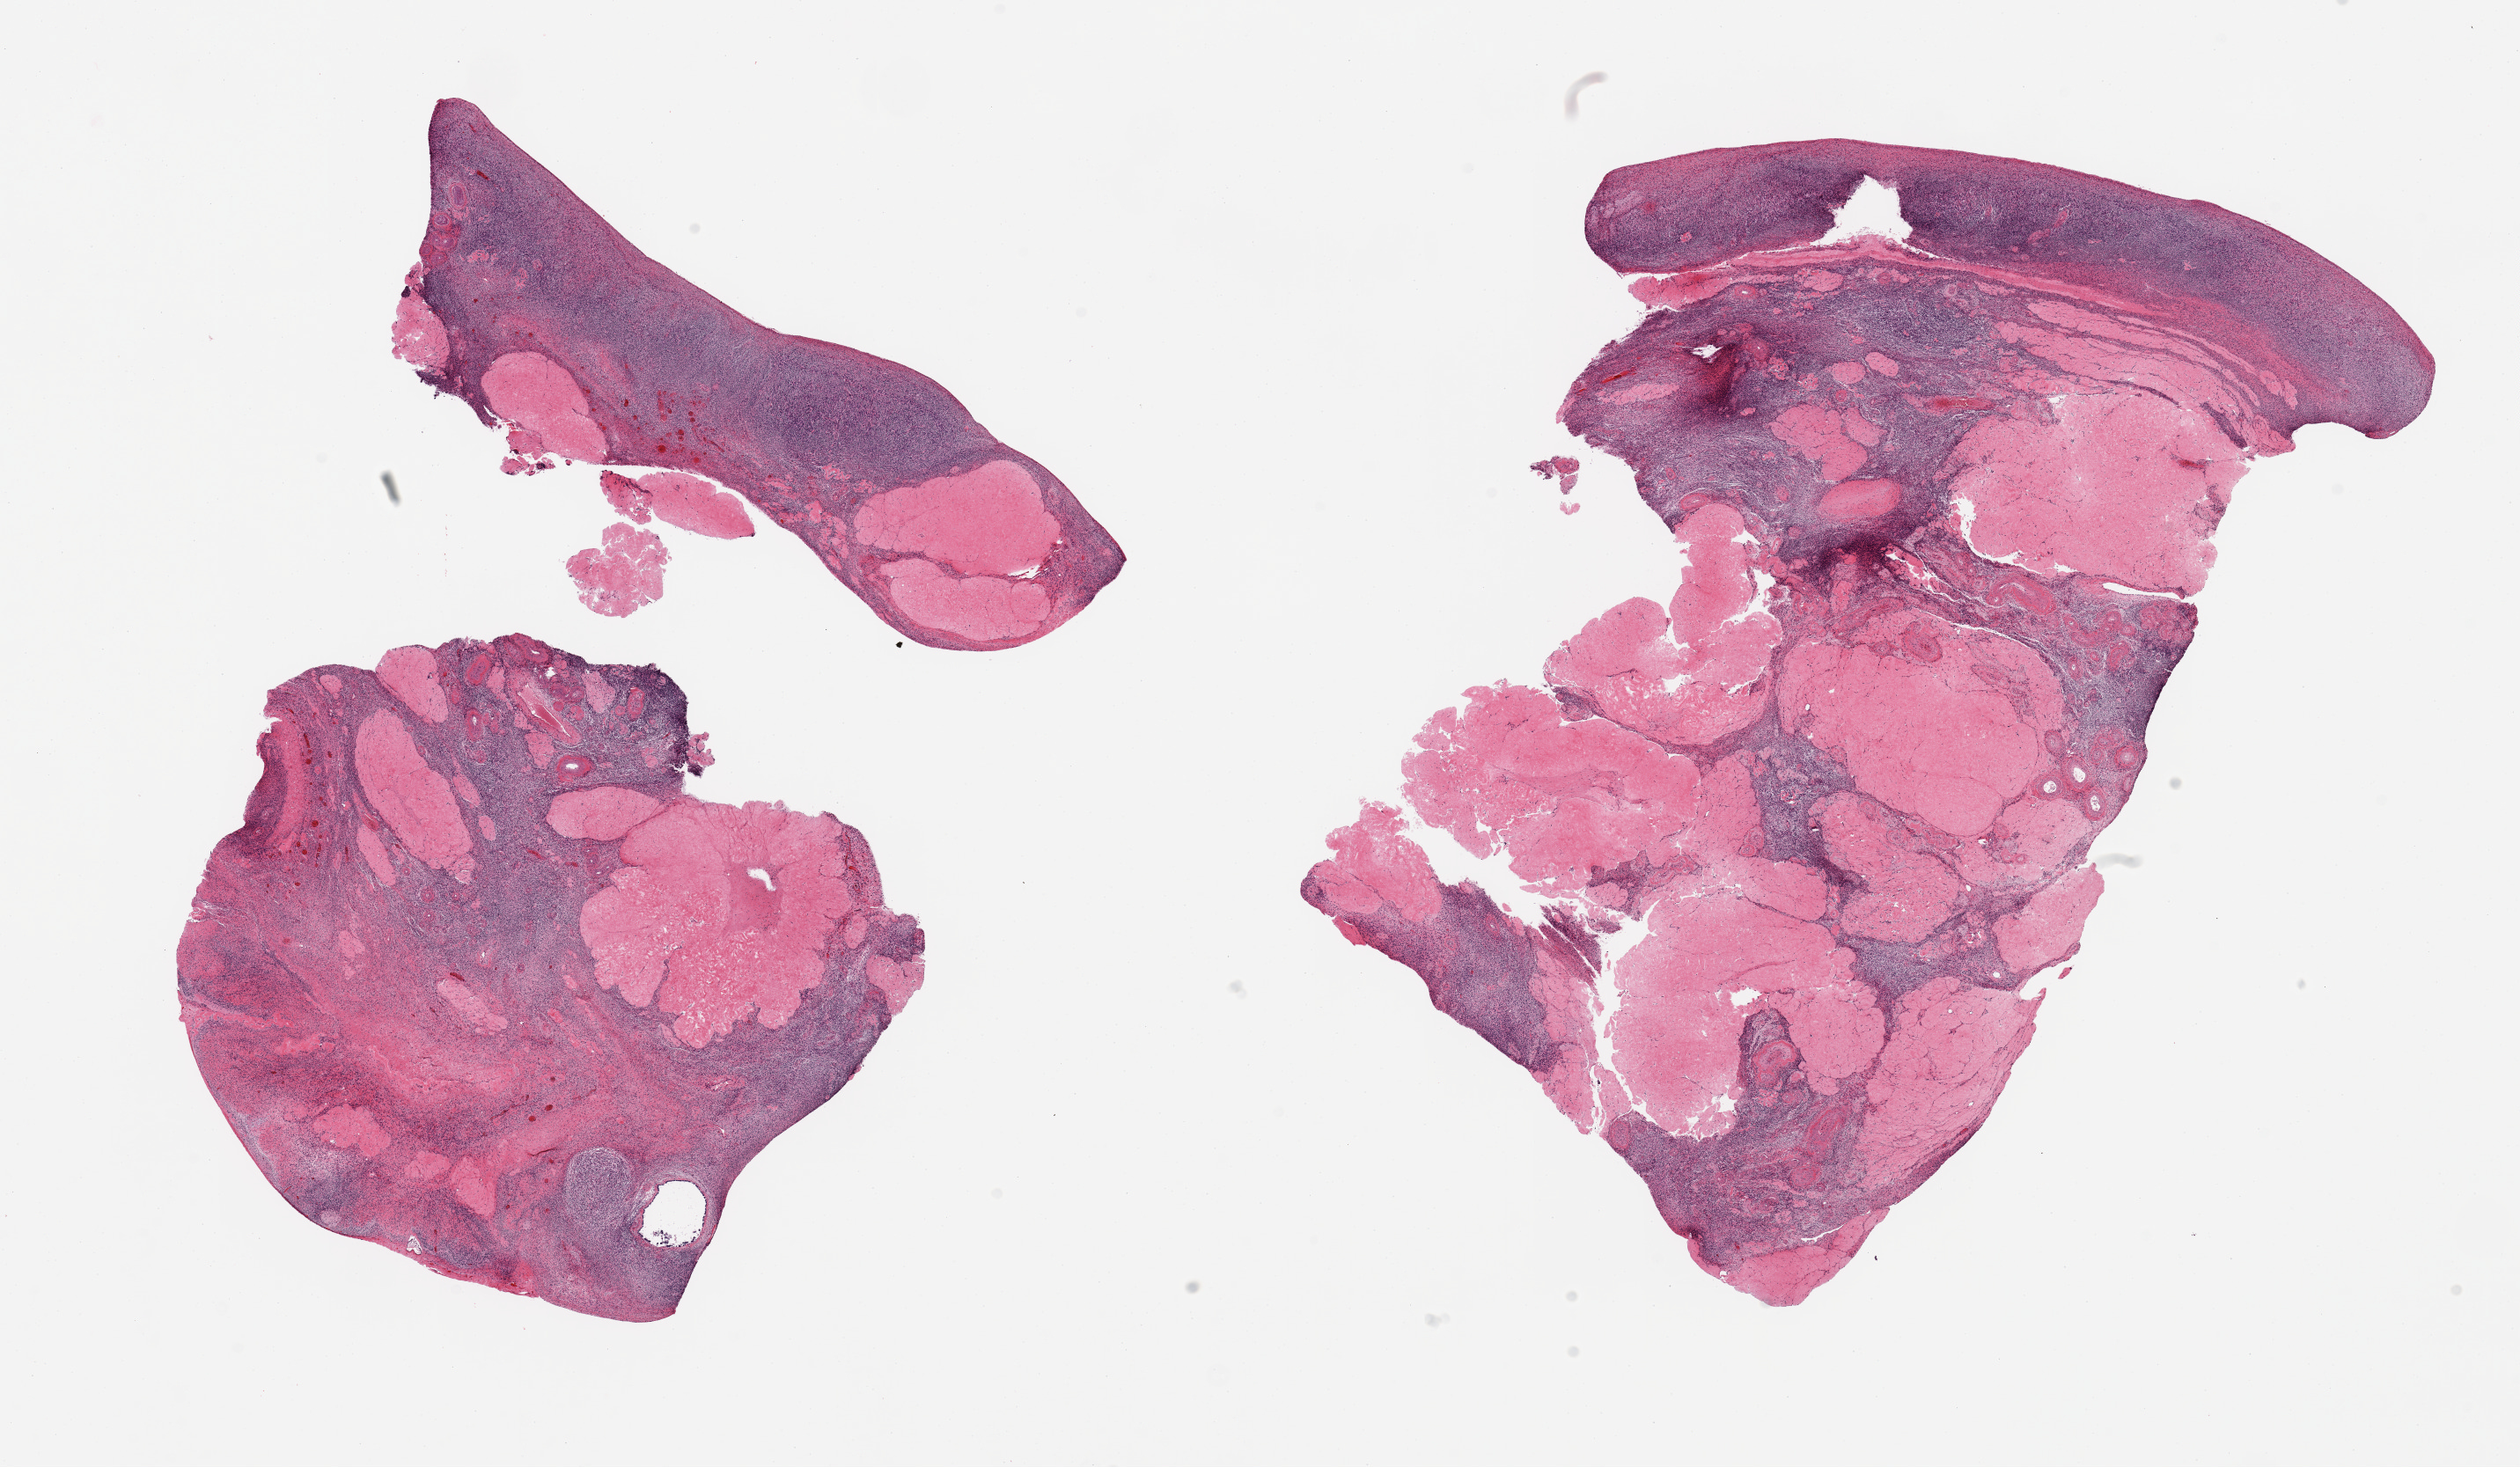
Whole-slide image, haematoxylin and eosin stain, brightfield — low-resolution overview of the scanned area, about 22.6 x 13.2 mm; PAXgene-fixed, paraffin-embedded tissue; sampled site (target tissue): ovary; tissue donor sample. Donor: female.
Pathologist's review note for this sample: 2 pieces, post menopausal involution.